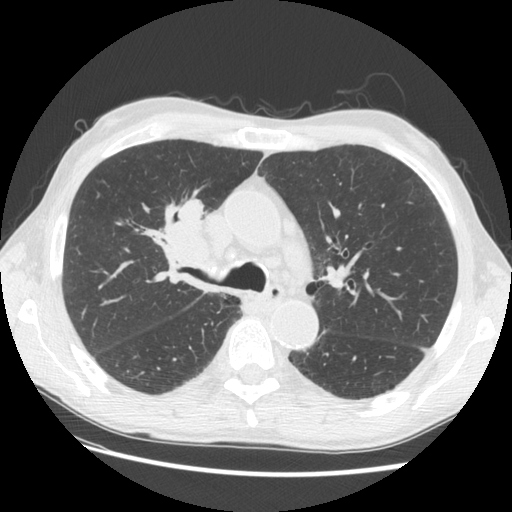
Low-dose screening chest CT, one axial slice; slice 89 of 133 in the series (ordered by position); 120 kVp; lung window (W 1500 / L -600 HU); 2.5 mm slice thickness; 512 × 512 image matrix, field of view 360 × 360 mm.
Annotated regions visible in this slice (manually delineated by an expert):
- lesion 1 (tumor, hilum of right lung): bounding box (x1, y1, x2, y2) in pixels: (164, 198, 209, 262)